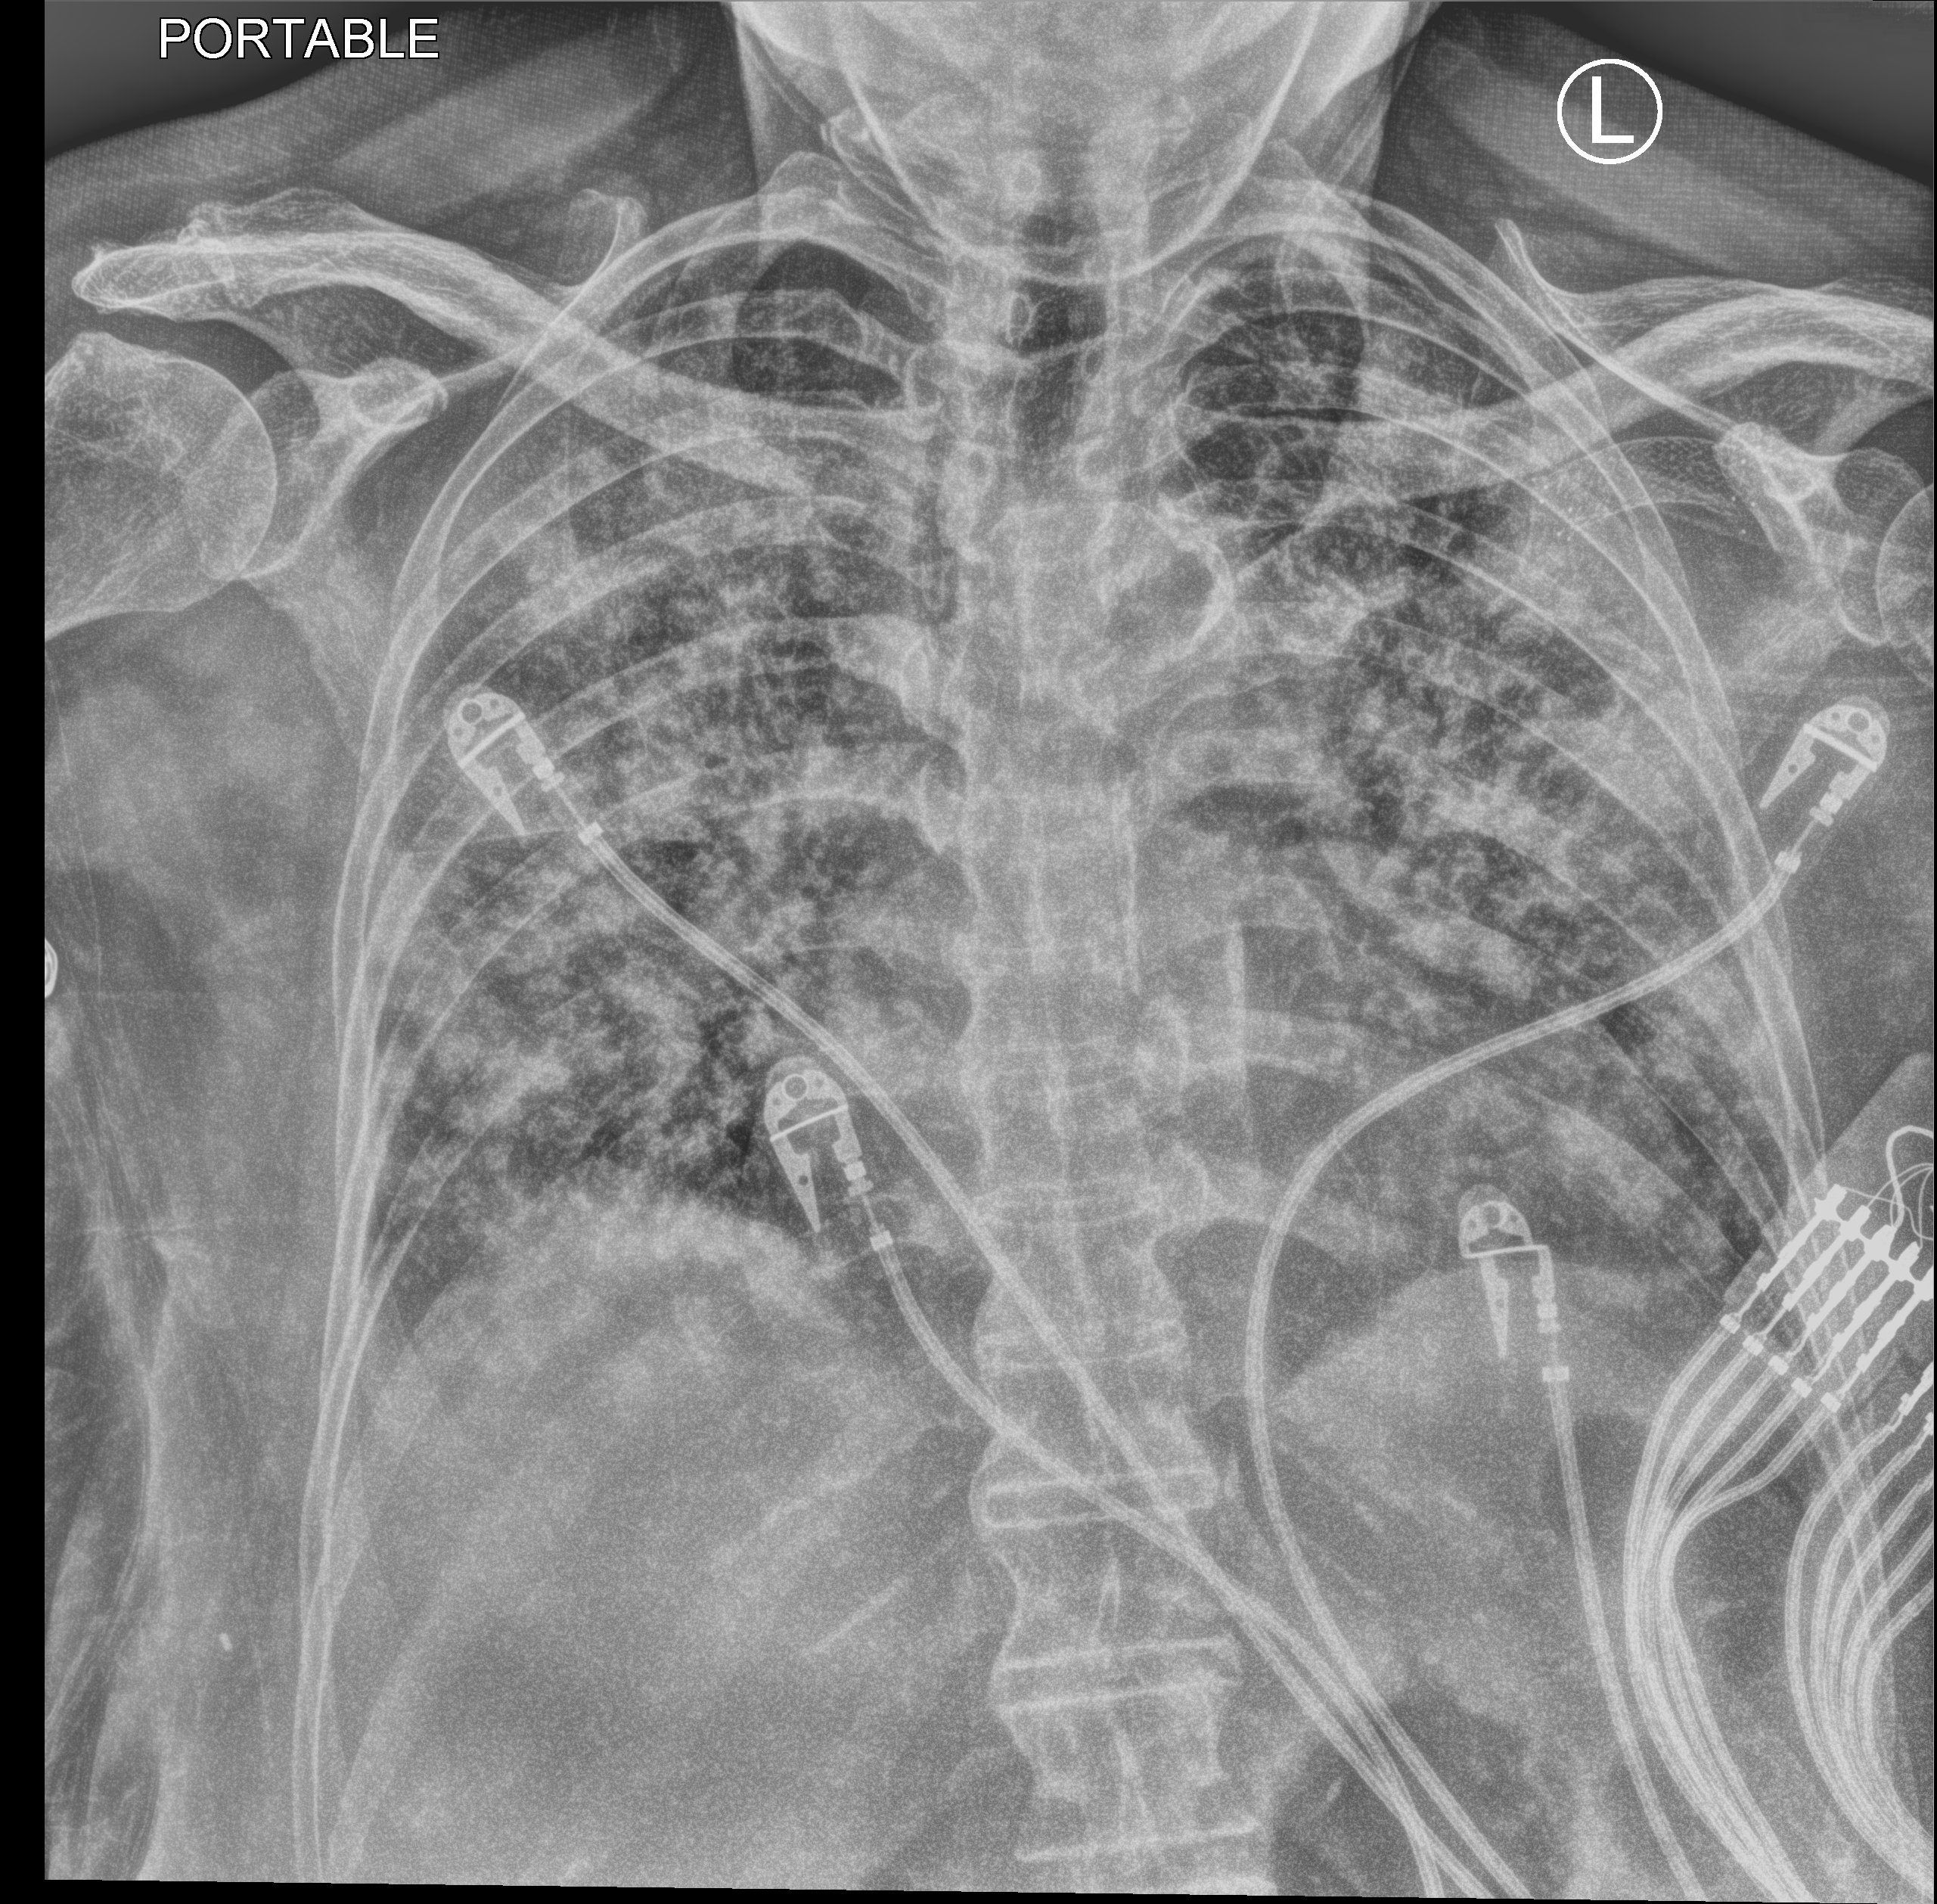
Chest X-ray (portable); anteroposterior (AP) projection. Patient hospitalised with COVID-19; female, aged 60–74 years.
Admission-level facts for this patient (not findings on this image; timing relative to this image not recorded):
- mechanically ventilated during this hospital stay: yes